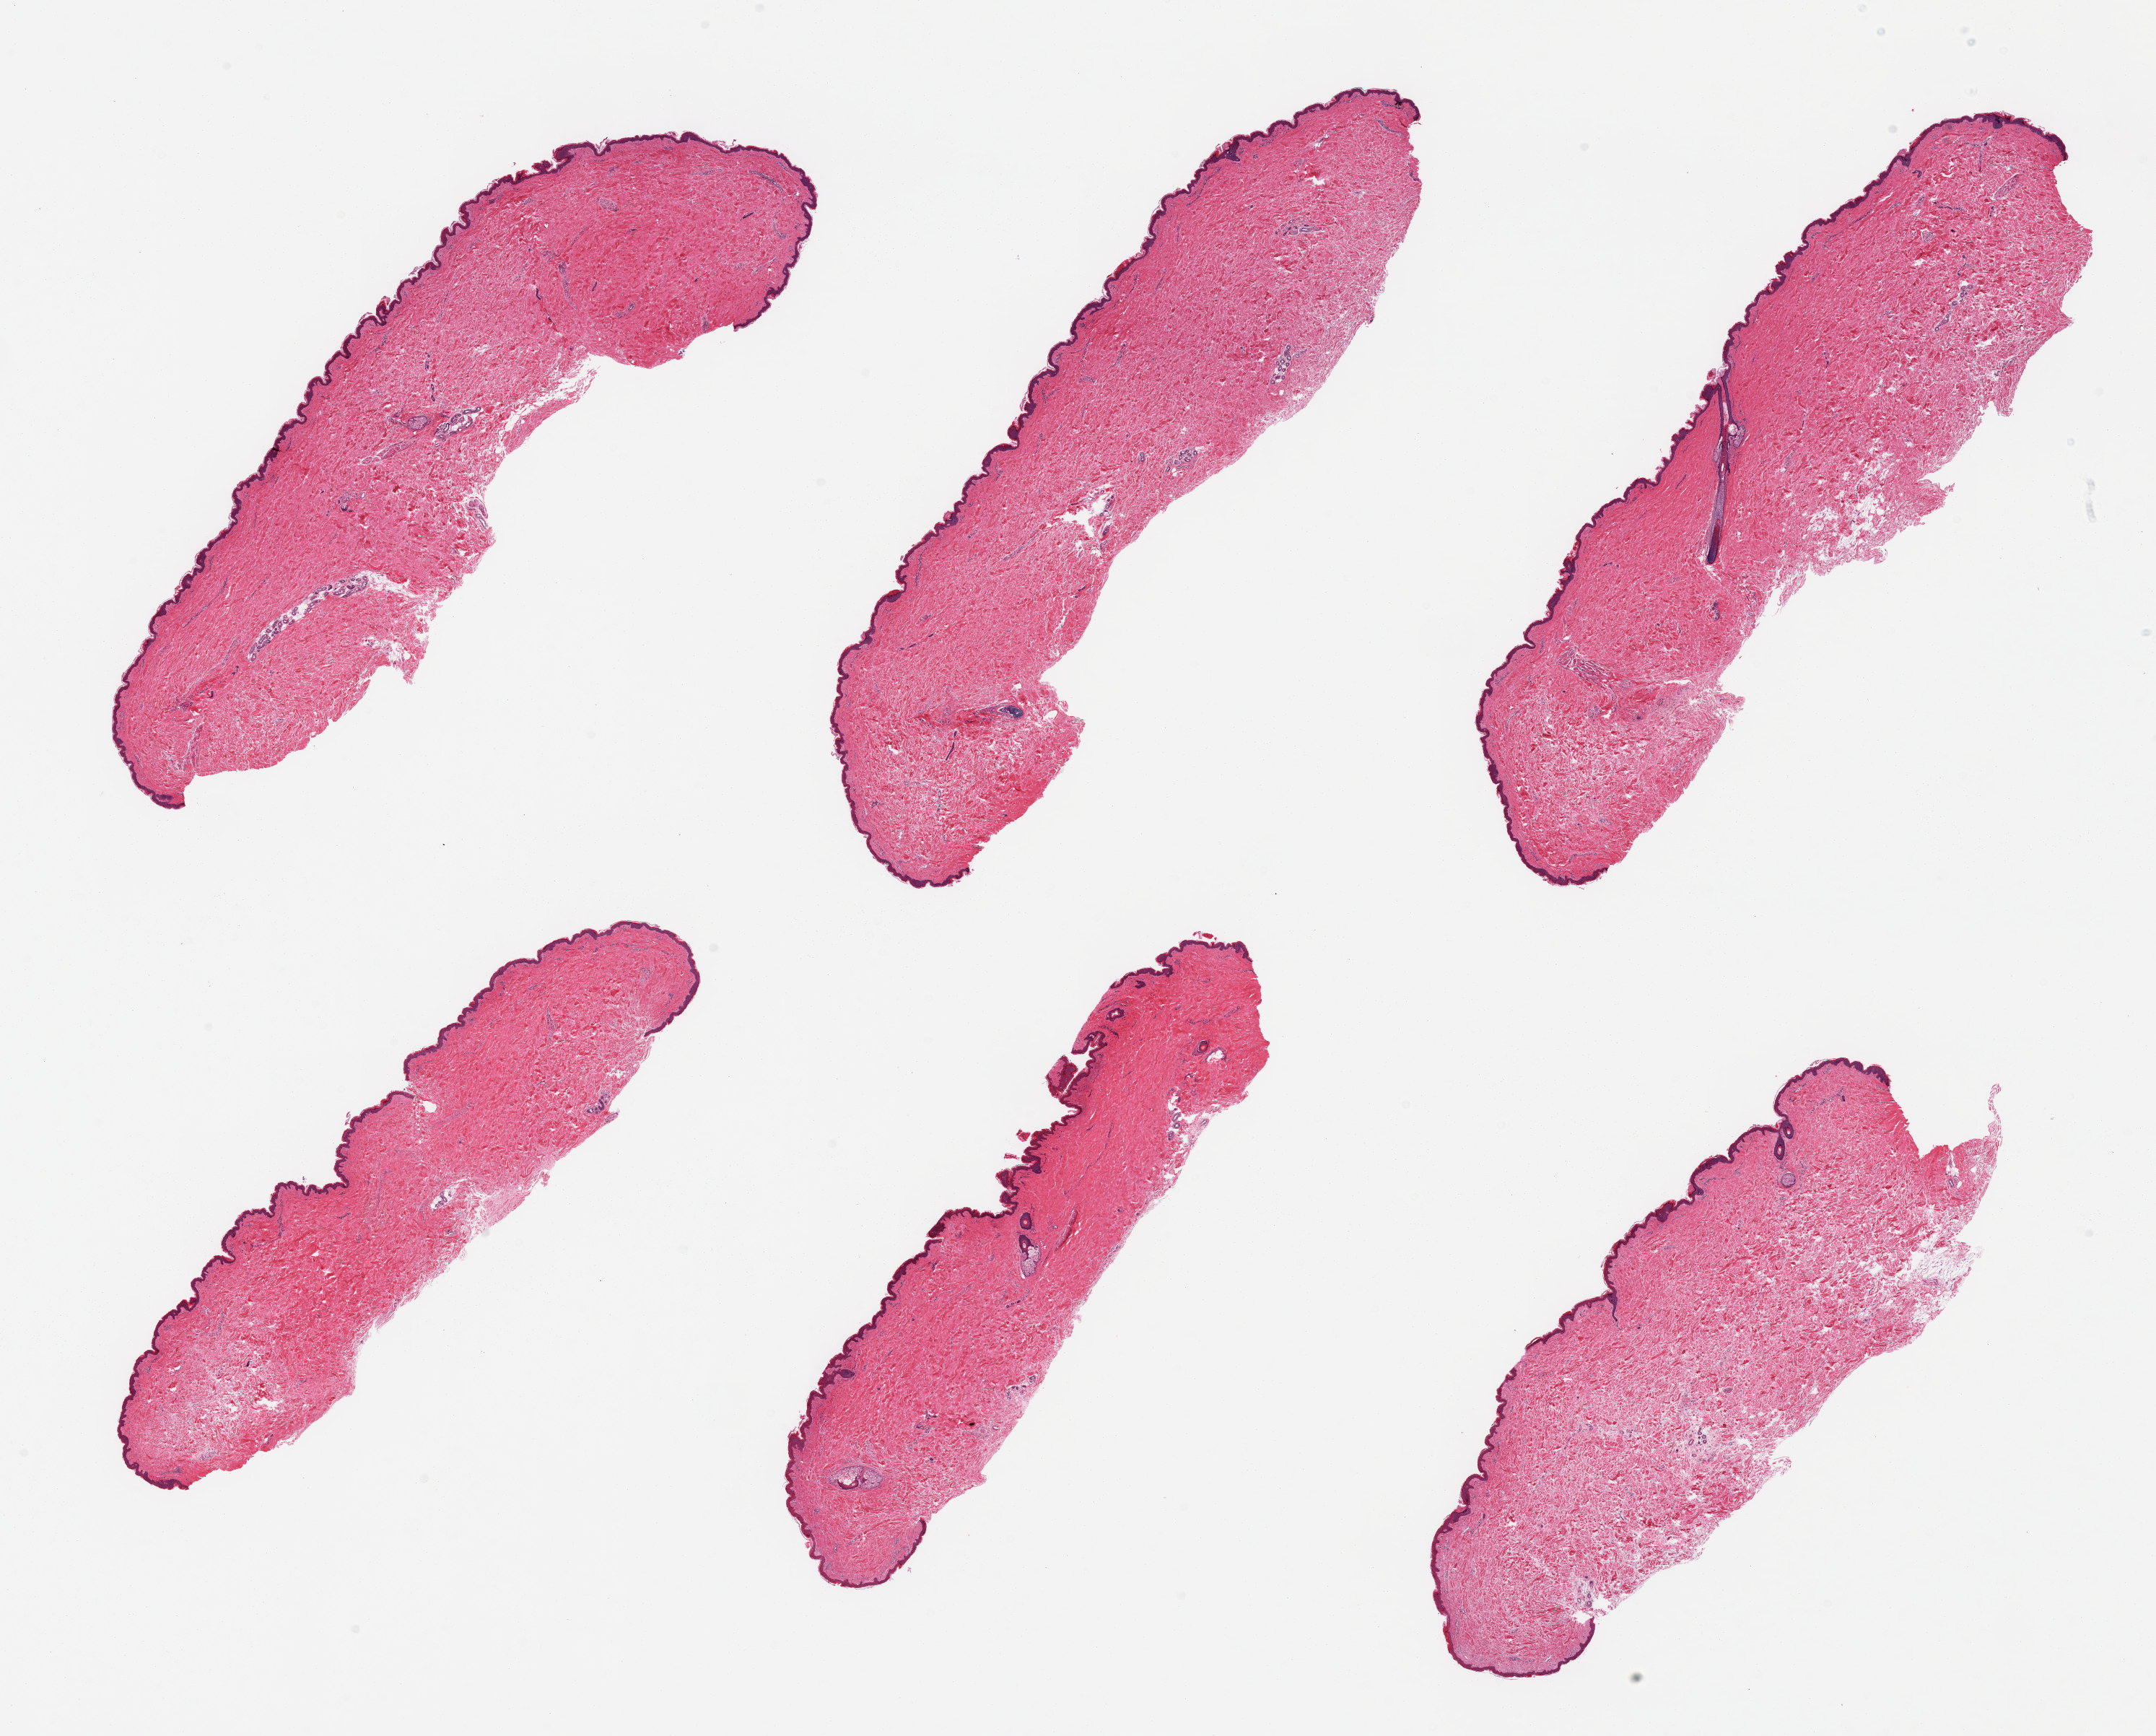
Haematoxylin and eosin whole-slide image, brightfield, low-resolution overview of the scanned area, about 23.6 x 19.0 mm (acquisition: 20x scan), PAXgene-fixed paraffin-embedded (PFPE) section, section of skin of suprapubic region (target tissue), donor tissue sample.
• pathologist's review note for this sample: 6 pieces; well trimmed; <5% dermal fat